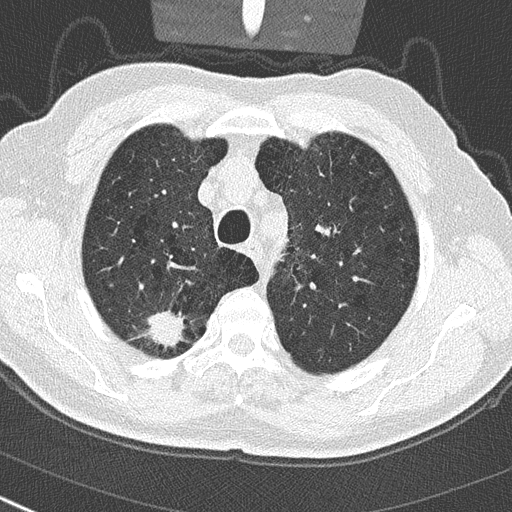
Low-dose screening chest CT, one axial slice. Slice 231 of 290 in the series (ordered by position). Reconstruction kernel B50f. Lung window (W 1500 / L -600 HU). 512 × 512 image matrix, field of view 300 × 300 mm.
Annotated regions visible in this slice (manually delineated by an expert):
- lesion 1 (tumor, upper lobe of right lung): bounding box [x1, y1, x2, y2] px = [149, 309, 185, 351]